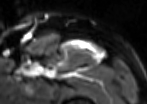
MRI of an extremity soft-tissue mass, one axial slice; slice 80 of 85 in the series (ordered by position); T2-weighted fat-saturated; MR volume resampled by the dataset authors to the PET/CT grid (not the native acquisition matrix); 147 × 104 image matrix, field of view 144 × 102 mm. Male patient. Case-level facts recorded for this patient, not image findings: histological type: extraskeletal osteosarcoma; grade: high; site of the primary tumour: thigh.
Annotated regions visible in this slice (expert contour drawn on MRI and transferred to this co-registered scan by the dataset authors):
- gross tumour volume (mass): box from (x=99, y=49) to (x=105, y=59) px